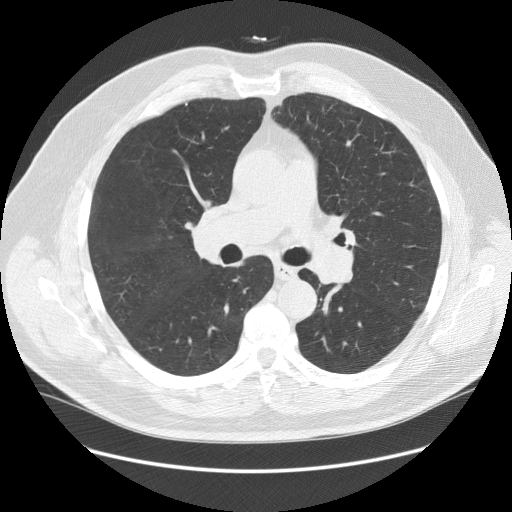
Axial slice from a low-dose chest CT screening exam; baseline screening round; lung window (W 1500 / L -600 HU); standard (soft-tissue) reconstruction kernel (STANDARD); slice 58 of 140 in the series. Male, age 64 years at enrolment. Former smoker at enrolment.
Lesion marked by an expert reader, bounding box <180,193,247,267> (left, top, right, bottom; pixels). Screening reader's record for this exam (one nodule recorded; not confirmed to be the boxed lesion): non-calcified nodule or mass ≥4 mm, right lower lobe, 7 × 5 mm, smooth margins, soft tissue attenuation. Lung cancer was diagnosed 456 days after this screen: adenocarcinoma, NOS, right upper lobe, poorly differentiated (G3), stage IB (AJCC 6th edition), 37 mm at pathology.